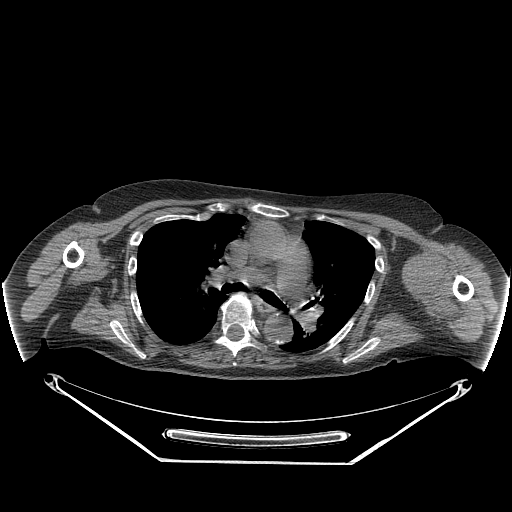
CT of an extremity soft-tissue mass (from a PET/CT study), one axial slice; slice 182 of 267 in the series (ordered by position); soft-tissue window (W 400 / L 40 HU); 3.75 mm slice thickness; 512 × 512 image matrix, field of view 500 × 500 mm. Female patient. Case-level facts recorded for this patient, not image findings: histological type: pleiomorphic leiomyosarcoma; grade: high; site of the primary tumour: left biceps.
Structures marked on this image (expert contour drawn on MRI and transferred to this co-registered scan by the dataset authors):
- gross tumour volume including surrounding oedema: box from (x=409, y=253) to (x=449, y=309) px
- gross tumour volume (mass): (x=409, y=253)–(x=449, y=298)